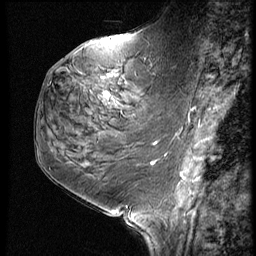
Breast MRI (dynamic contrast-enhanced), one sagittal slice; slice 28 of 60 in the series (ordered by position); 3 images stored at this slice position (order not interpretable as contrast timing); 1.5 T; TE 4.2 ms, TR 9 ms; 256 × 256 image matrix, field of view 180 × 180 mm. Patient: female, 59 years. Case-level facts recorded for this patient, not image findings: setting: breast cancer imaged before/during neoadjuvant chemotherapy; receptor status: HER2-positive.
Annotated regions visible in this slice (semi-automatically segmented with operator editing):
- analysis volume of interest (the breast-tissue region the enhancement analysis was run in; not a lesion): bounding box (x1, y1, x2, y2) in pixels: (78, 61, 161, 125)
- tumour enhancement mask (voxels above the 140 % enhancement threshold inside the analysis volume of interest): (105, 93, 108, 96)